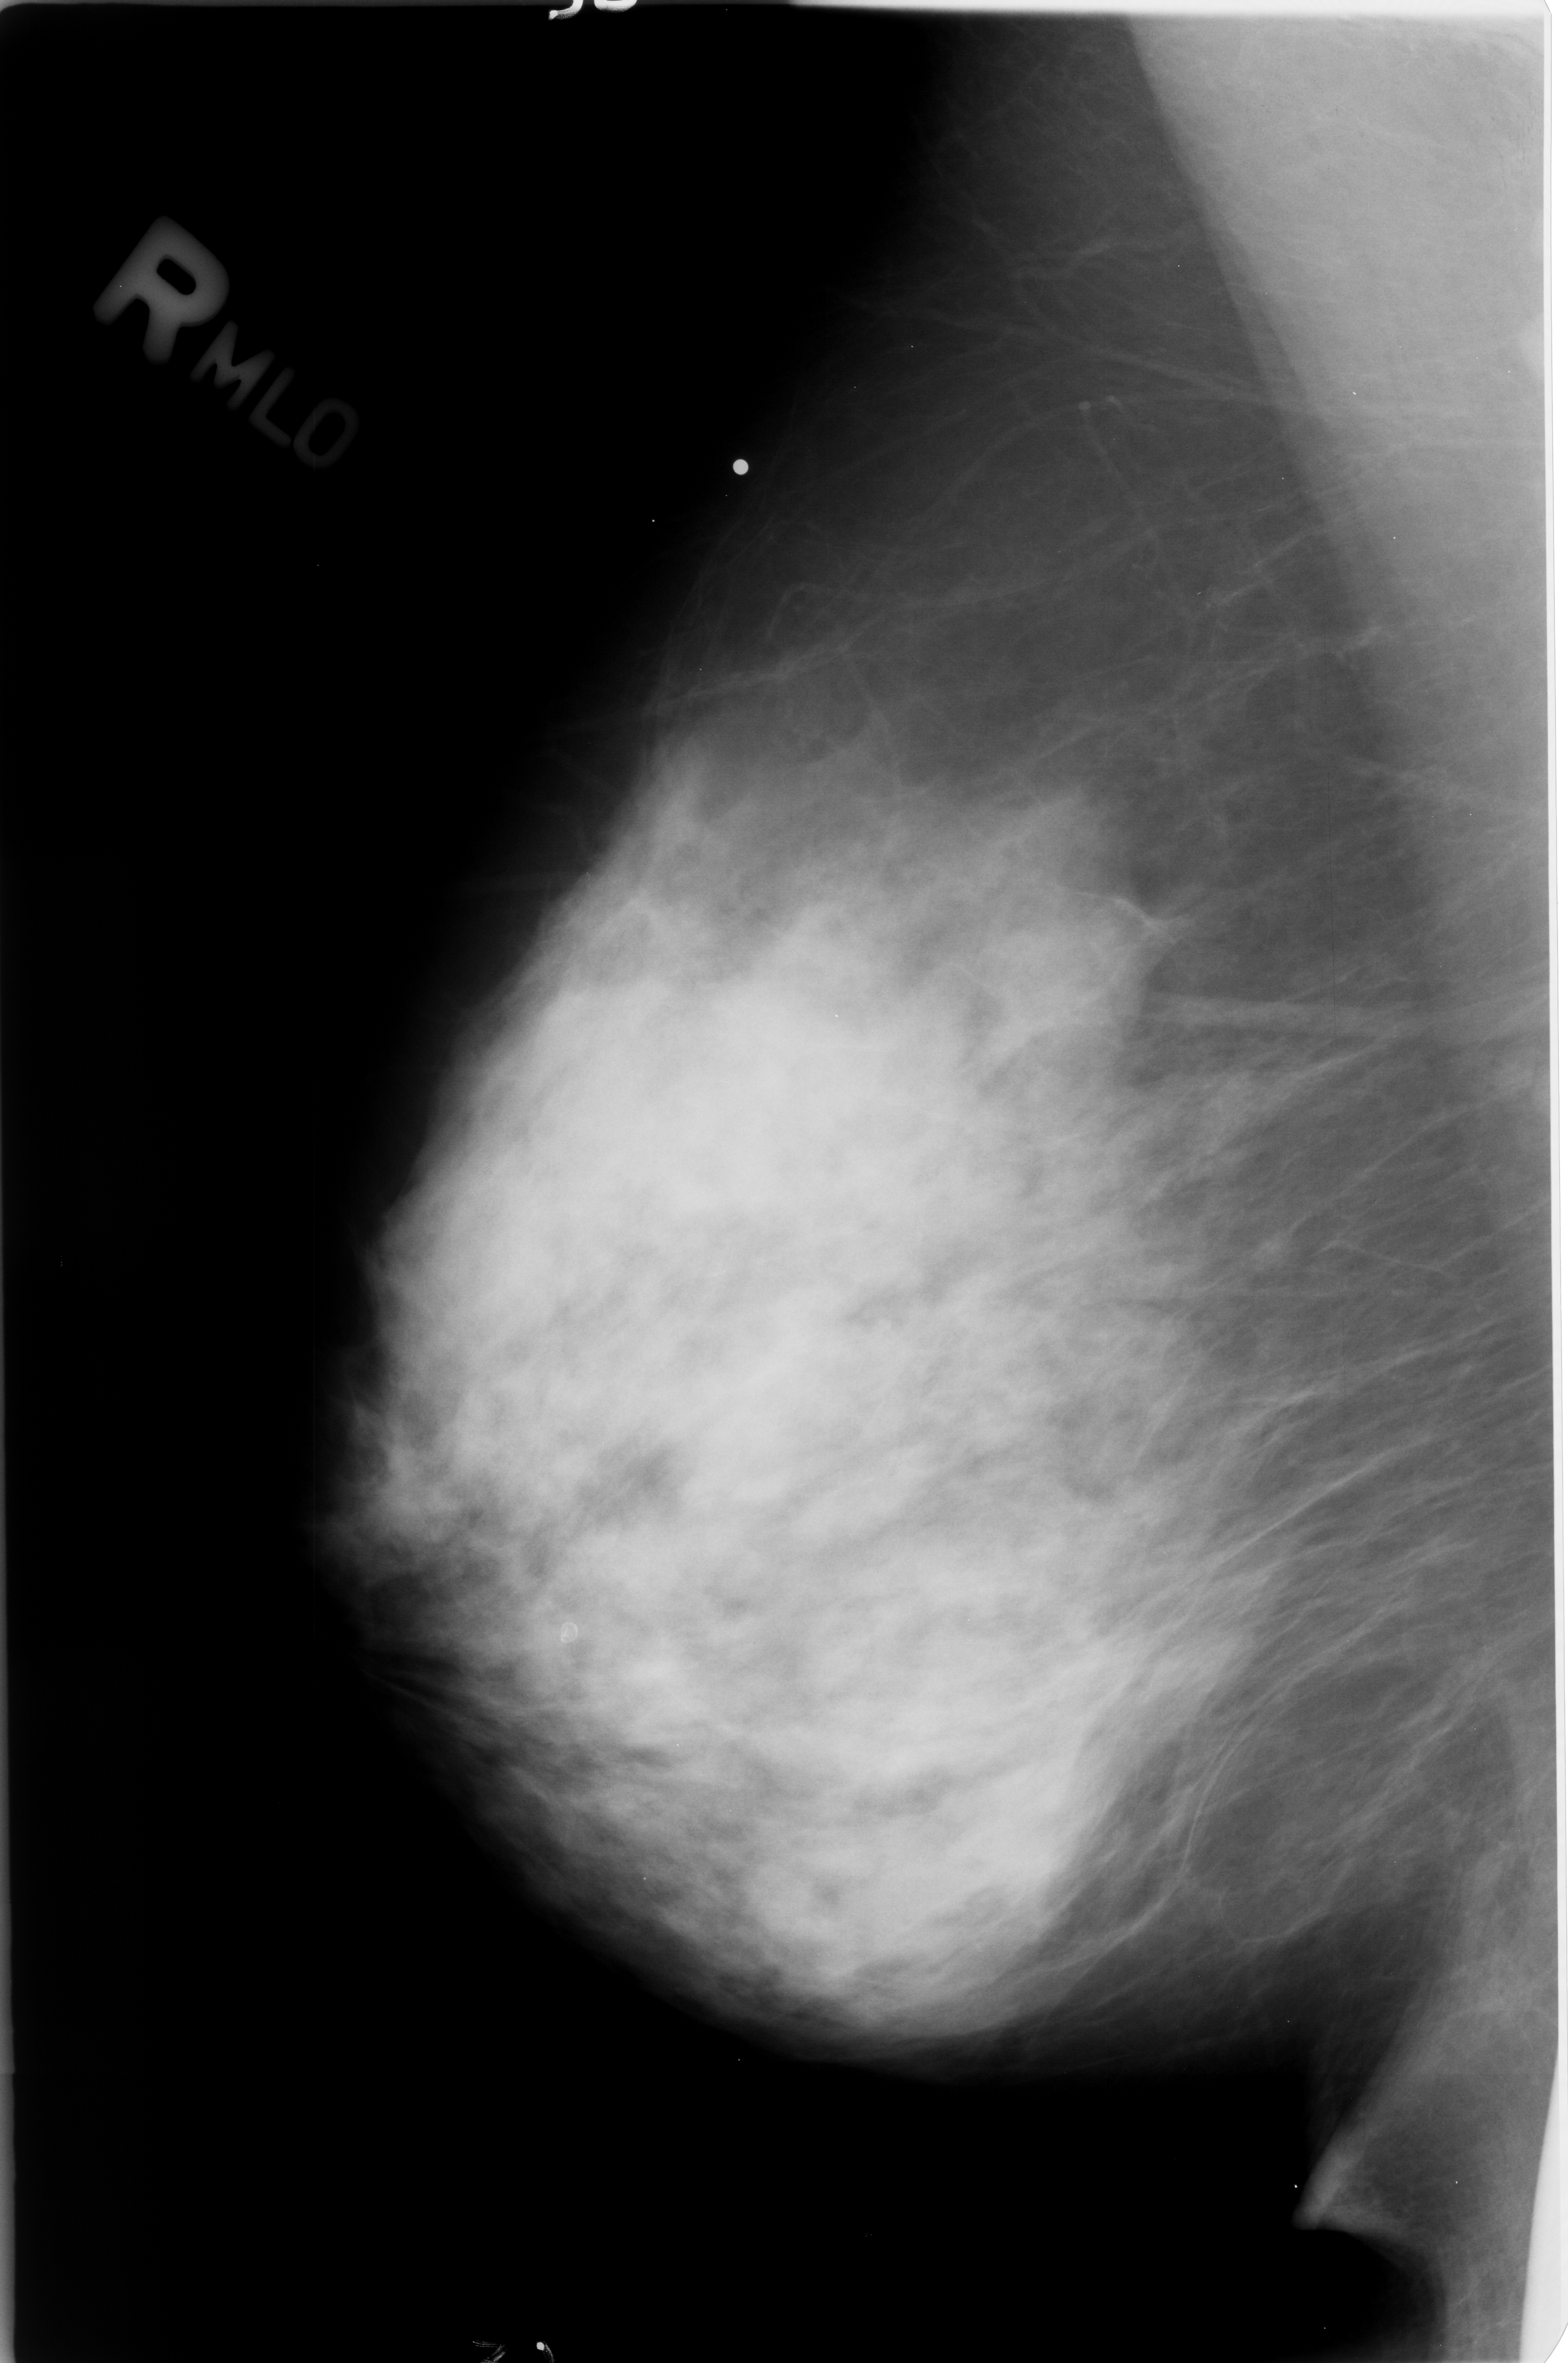
Digitized screen-film mammogram, right breast, MLO view, BI-RADS breast density category 4 (scale 1–4).
Marked abnormality: calcifications, morphology lucent center; BI-RADS assessment category 2; subtlety rating 3 on a 1 (subtle) to 5 (obvious) scale; benign; no additional work-up was recommended (benign without callback).